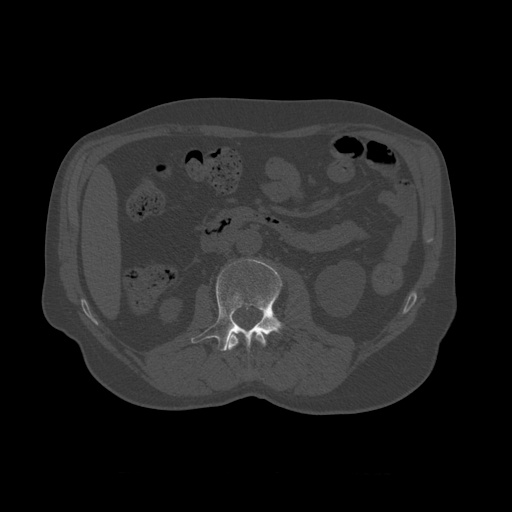
CT including the spine, one axial slice; position 331 of 450 along the scan axis; reconstruction kernel STANDARD; 120 kVp; bone window (W 1800 / L 400 HU); 1.25 mm slice thickness; 512 × 512 image matrix, field of view 405 × 405 mm. Patient age 75 years. From the clinical record (not read from this slice): primary cancer: prostate.
Structures marked on this image (semi-automatically segmented with operator editing):
- L1 vertebra: box from (x=226, y=331) to (x=267, y=351) px
- L2 vertebra: (x=191, y=259)–(x=285, y=352)